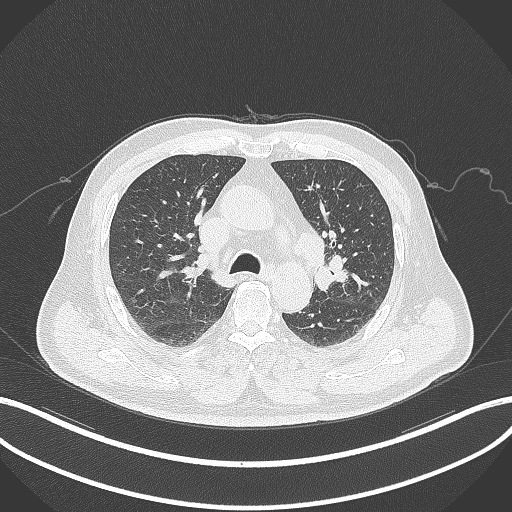
Chest CT, one axial slice; position 198 of 286 along the scan axis; reconstruction kernel B70f; 120 kVp; lung window (W 1500 / L -600 HU); 1 mm slice thickness; 512 × 512 image matrix, field of view 400 × 400 mm. Patient: male, 67 years. Case-level facts recorded for this patient, not image findings: clinical TNM (as recorded): T2a N1 M0.
Outlined on this slice (rectangle marked by the reading radiologist):
- lung tumour (recorded histology: adenocarcinoma): box from (x=309, y=256) to (x=352, y=290) px